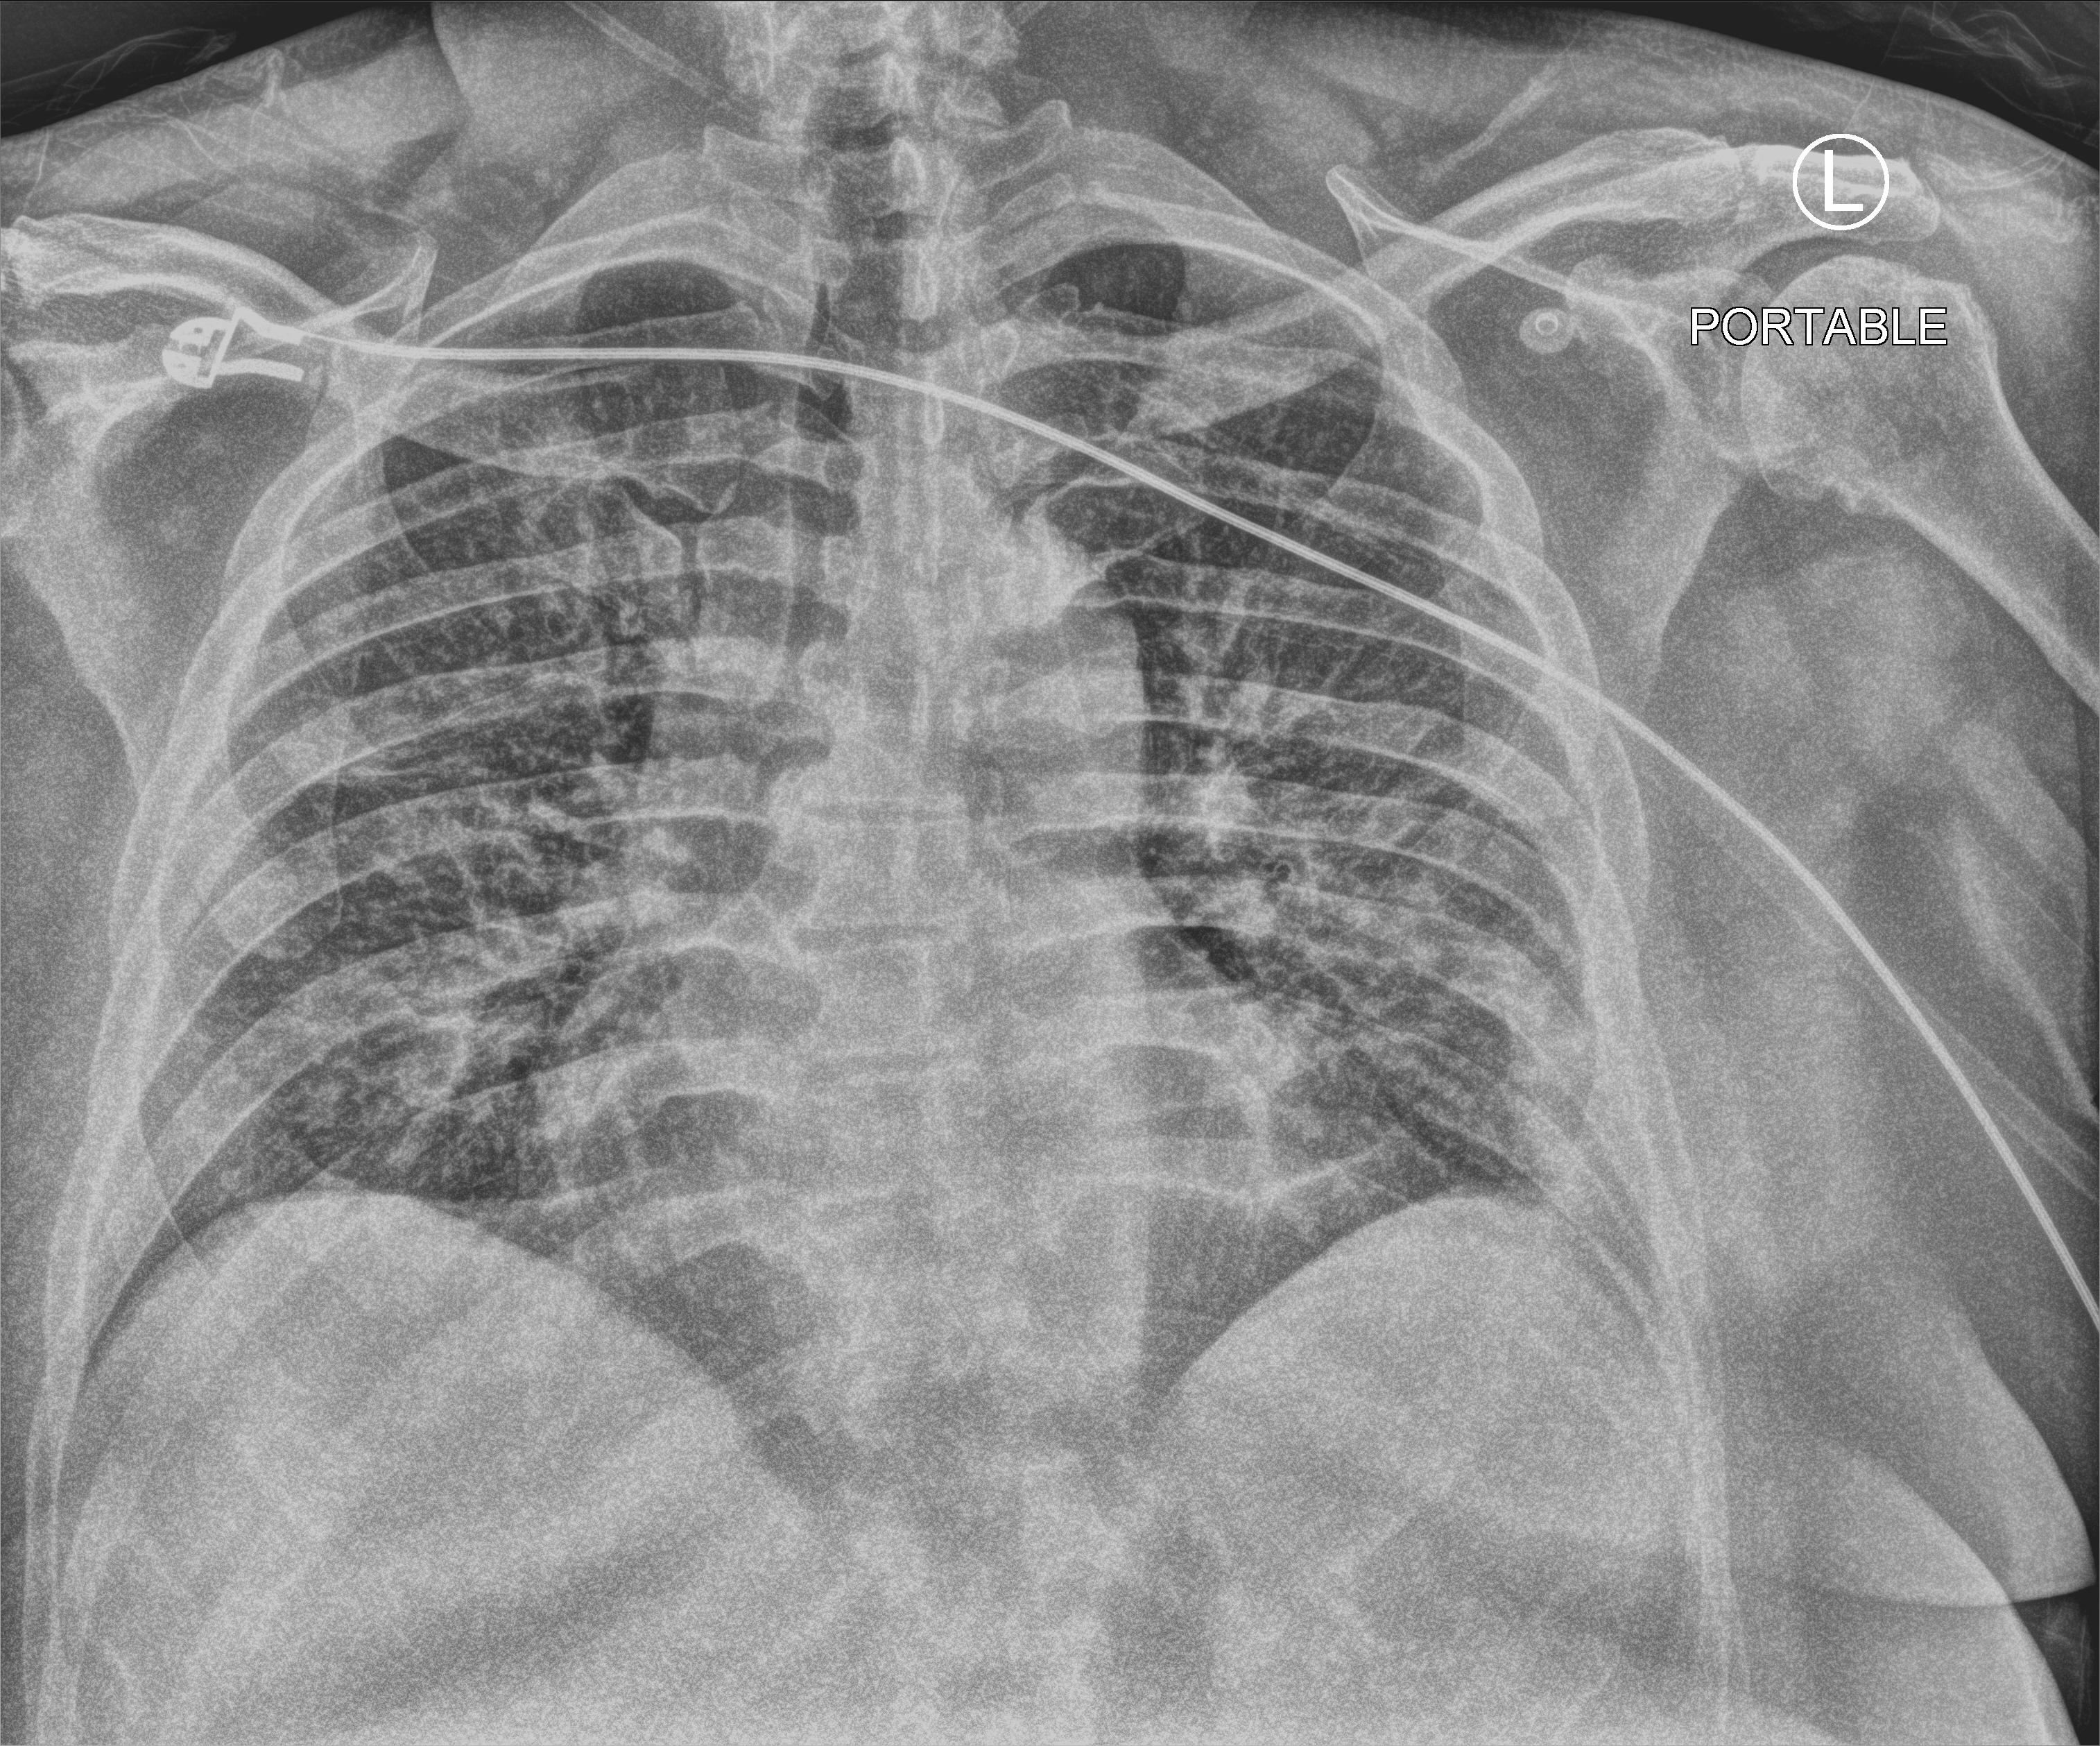
Chest X-ray (portable), anteroposterior (AP) projection. Patient hospitalised with COVID-19; male, aged 18–59 years.
Hospital-stay facts (about this admission, not read from this image; timing relative to this image not recorded):
- COPD (admission record): no
- mechanically ventilated during this hospital stay: yes
- chronic kidney disease (admission record): no